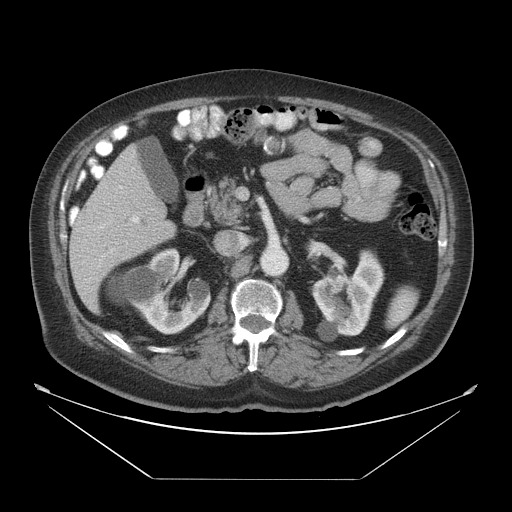
Contrast-enhanced abdominal CT, one axial slice; position 23 of 45 along the scan axis; reconstruction kernel STANDARD; soft-tissue window (W 400 / L 40 HU); 5 mm slice thickness; 512 × 512 image matrix. Male patient, age 87 years. Case-level facts recorded for this patient, not image findings: diagnosis: colorectal cancer liver metastases, imaged before liver resection; multiple liver metastases: no; largest metastasis: 4.5 cm.
Structures marked on this image (outlined manually by an expert reader):
- liver: bounding box [x1, y1, x2, y2] px = [70, 145, 177, 314]
- portal vein (with intrahepatic branches): [119, 186, 139, 223]